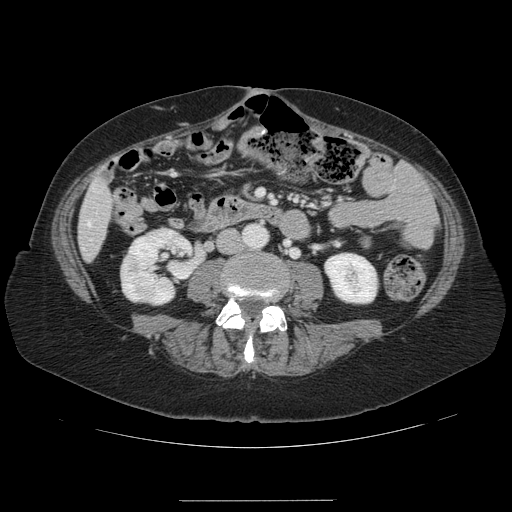
Contrast-enhanced abdominal CT, one axial slice; position 20 of 141 along the scan axis; intravenous contrast given; soft-tissue window (W 400 / L 40 HU); 2.5 mm slice thickness; 512 × 512 image matrix, field of view 393 × 393 mm. Female patient, age 74 years. Case-level facts recorded for this patient, not image findings: diagnosis: colorectal cancer liver metastases, imaged before liver resection; multiple liver metastases: yes; largest metastasis: 7 cm; disease in both lobes: yes.
Annotated regions visible in this slice (manually delineated by an expert):
- hepatic veins: bounding box (x1, y1, x2, y2) in pixels: (88, 223, 90, 225)
- liver: (79, 182, 112, 260)
- planned liver remnant (the part of the liver to remain after resection): (81, 197, 112, 260)